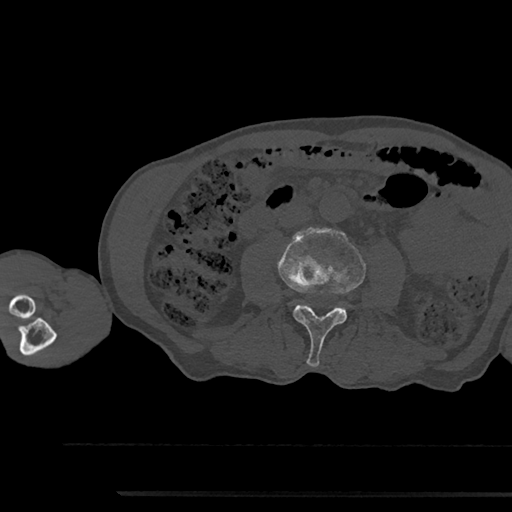
CT including the spine, one axial slice; reconstruction kernel Br40s/3; bone window (W 1800 / L 400 HU); 0.5 mm slice thickness; 512 × 512 image matrix. Male patient, age 79 years. From the clinical record (not read from this slice): primary cancer: prostate.
Annotated regions visible in this slice (semi-automatic segmentation, software-assisted and operator-edited):
- L3 vertebra: bounding box <278,228,366,367> (left, top, right, bottom; pixels)